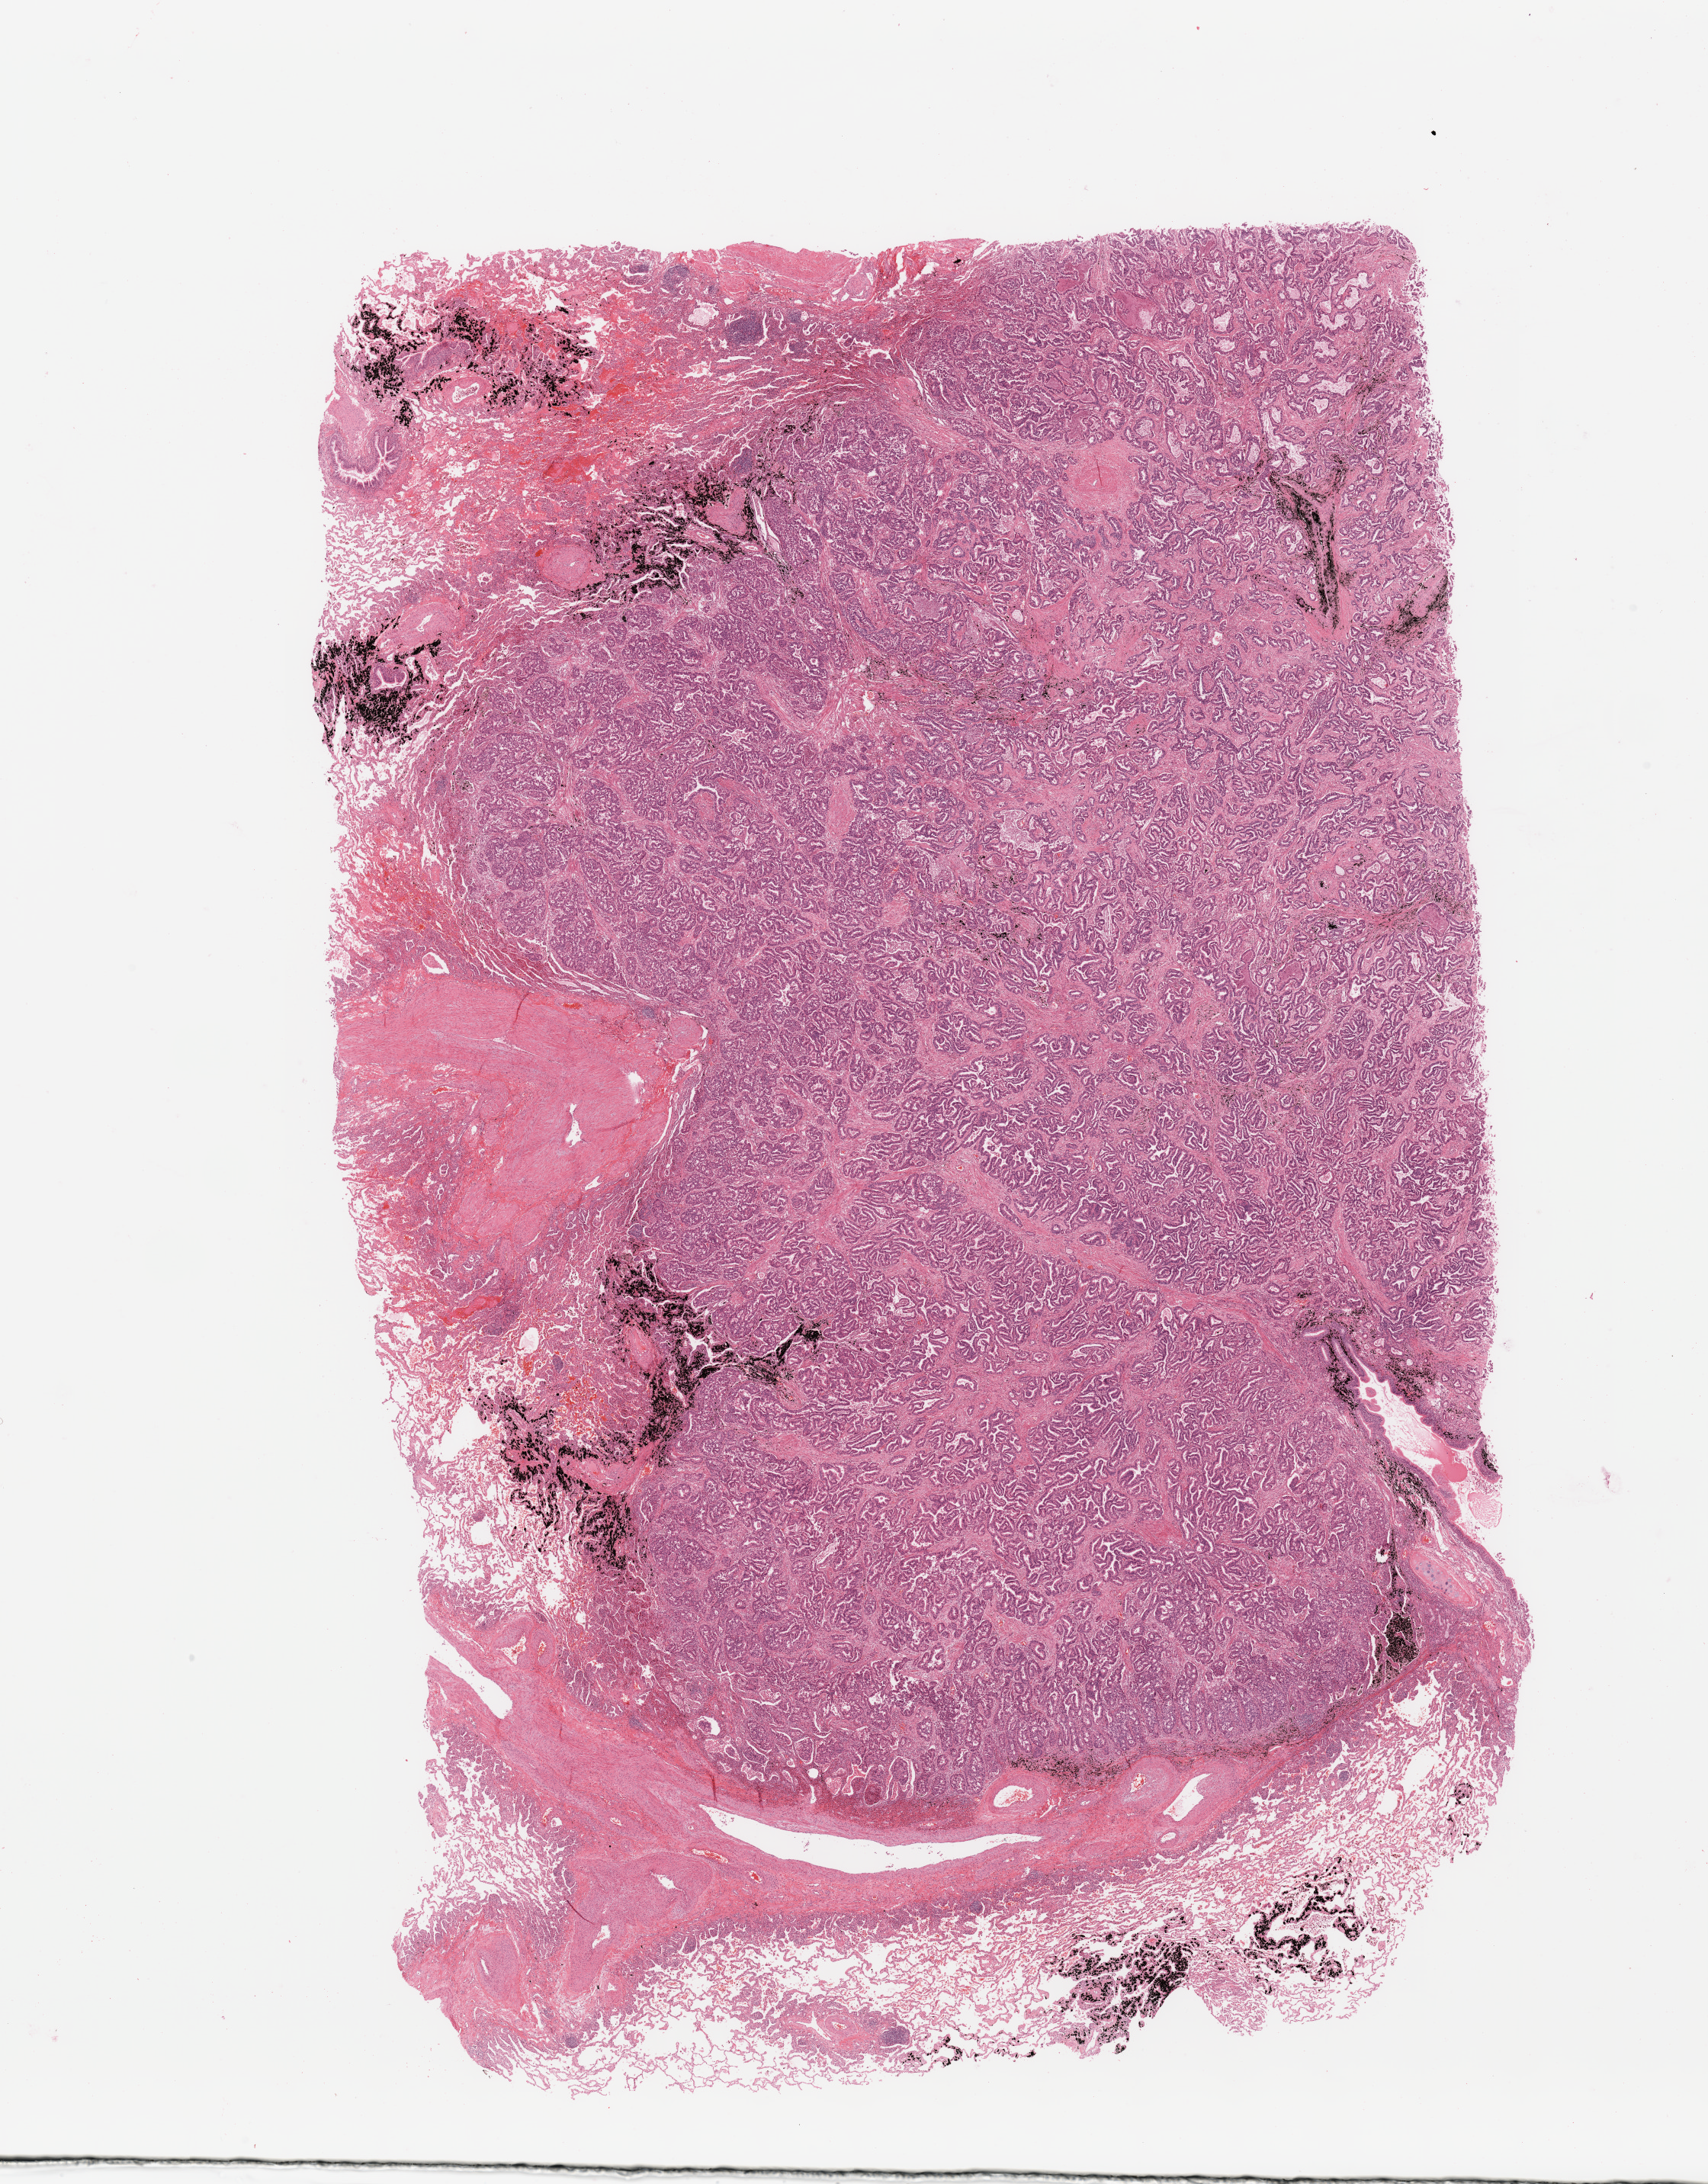
Digitized Hematoxylin and eosin (H&E) stained tissue section (whole slide) — whole scanned area (about 17.7 x 22.7 mm, acquisition: 20x scan) shown as a low-resolution overview; tumour tissue sample, lung. 59-year-old male patient.
Diagnosis: Adenocarcinoma, NOS.